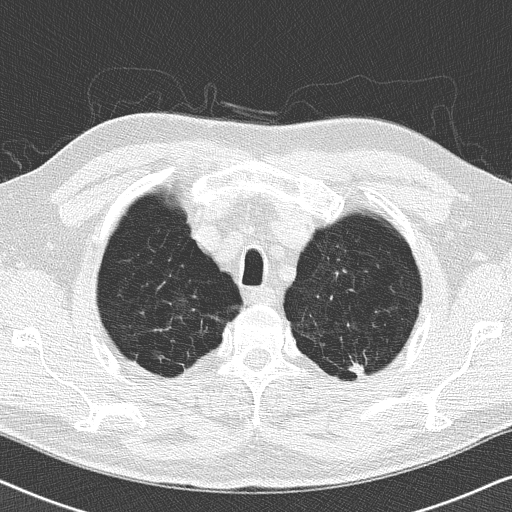
Chest CT (low-dose screening protocol), one axial image. Second annual screen. Lung window (W 1500 / L -600 HU). 2 mm slice thickness. Lung (sharp) reconstruction kernel (B50f). 512 × 512 image matrix. Male, age 62 years at enrolment.
Expert reader's lesion annotation, bounding box [x1, y1, x2, y2] px = [338, 352, 377, 386]. Reader record for this screening exam (exam-level; its link to the box is not recorded): non-calcified nodule or mass ≥4 mm, left upper lobe, 10 × 10 mm, soft tissue attenuation, pre-existing on the prior screen: yes; interval growth: no. Official screen result: positive, no significant change: stable abnormalities potentially related to lung cancer, unchanged since the prior screening exam.